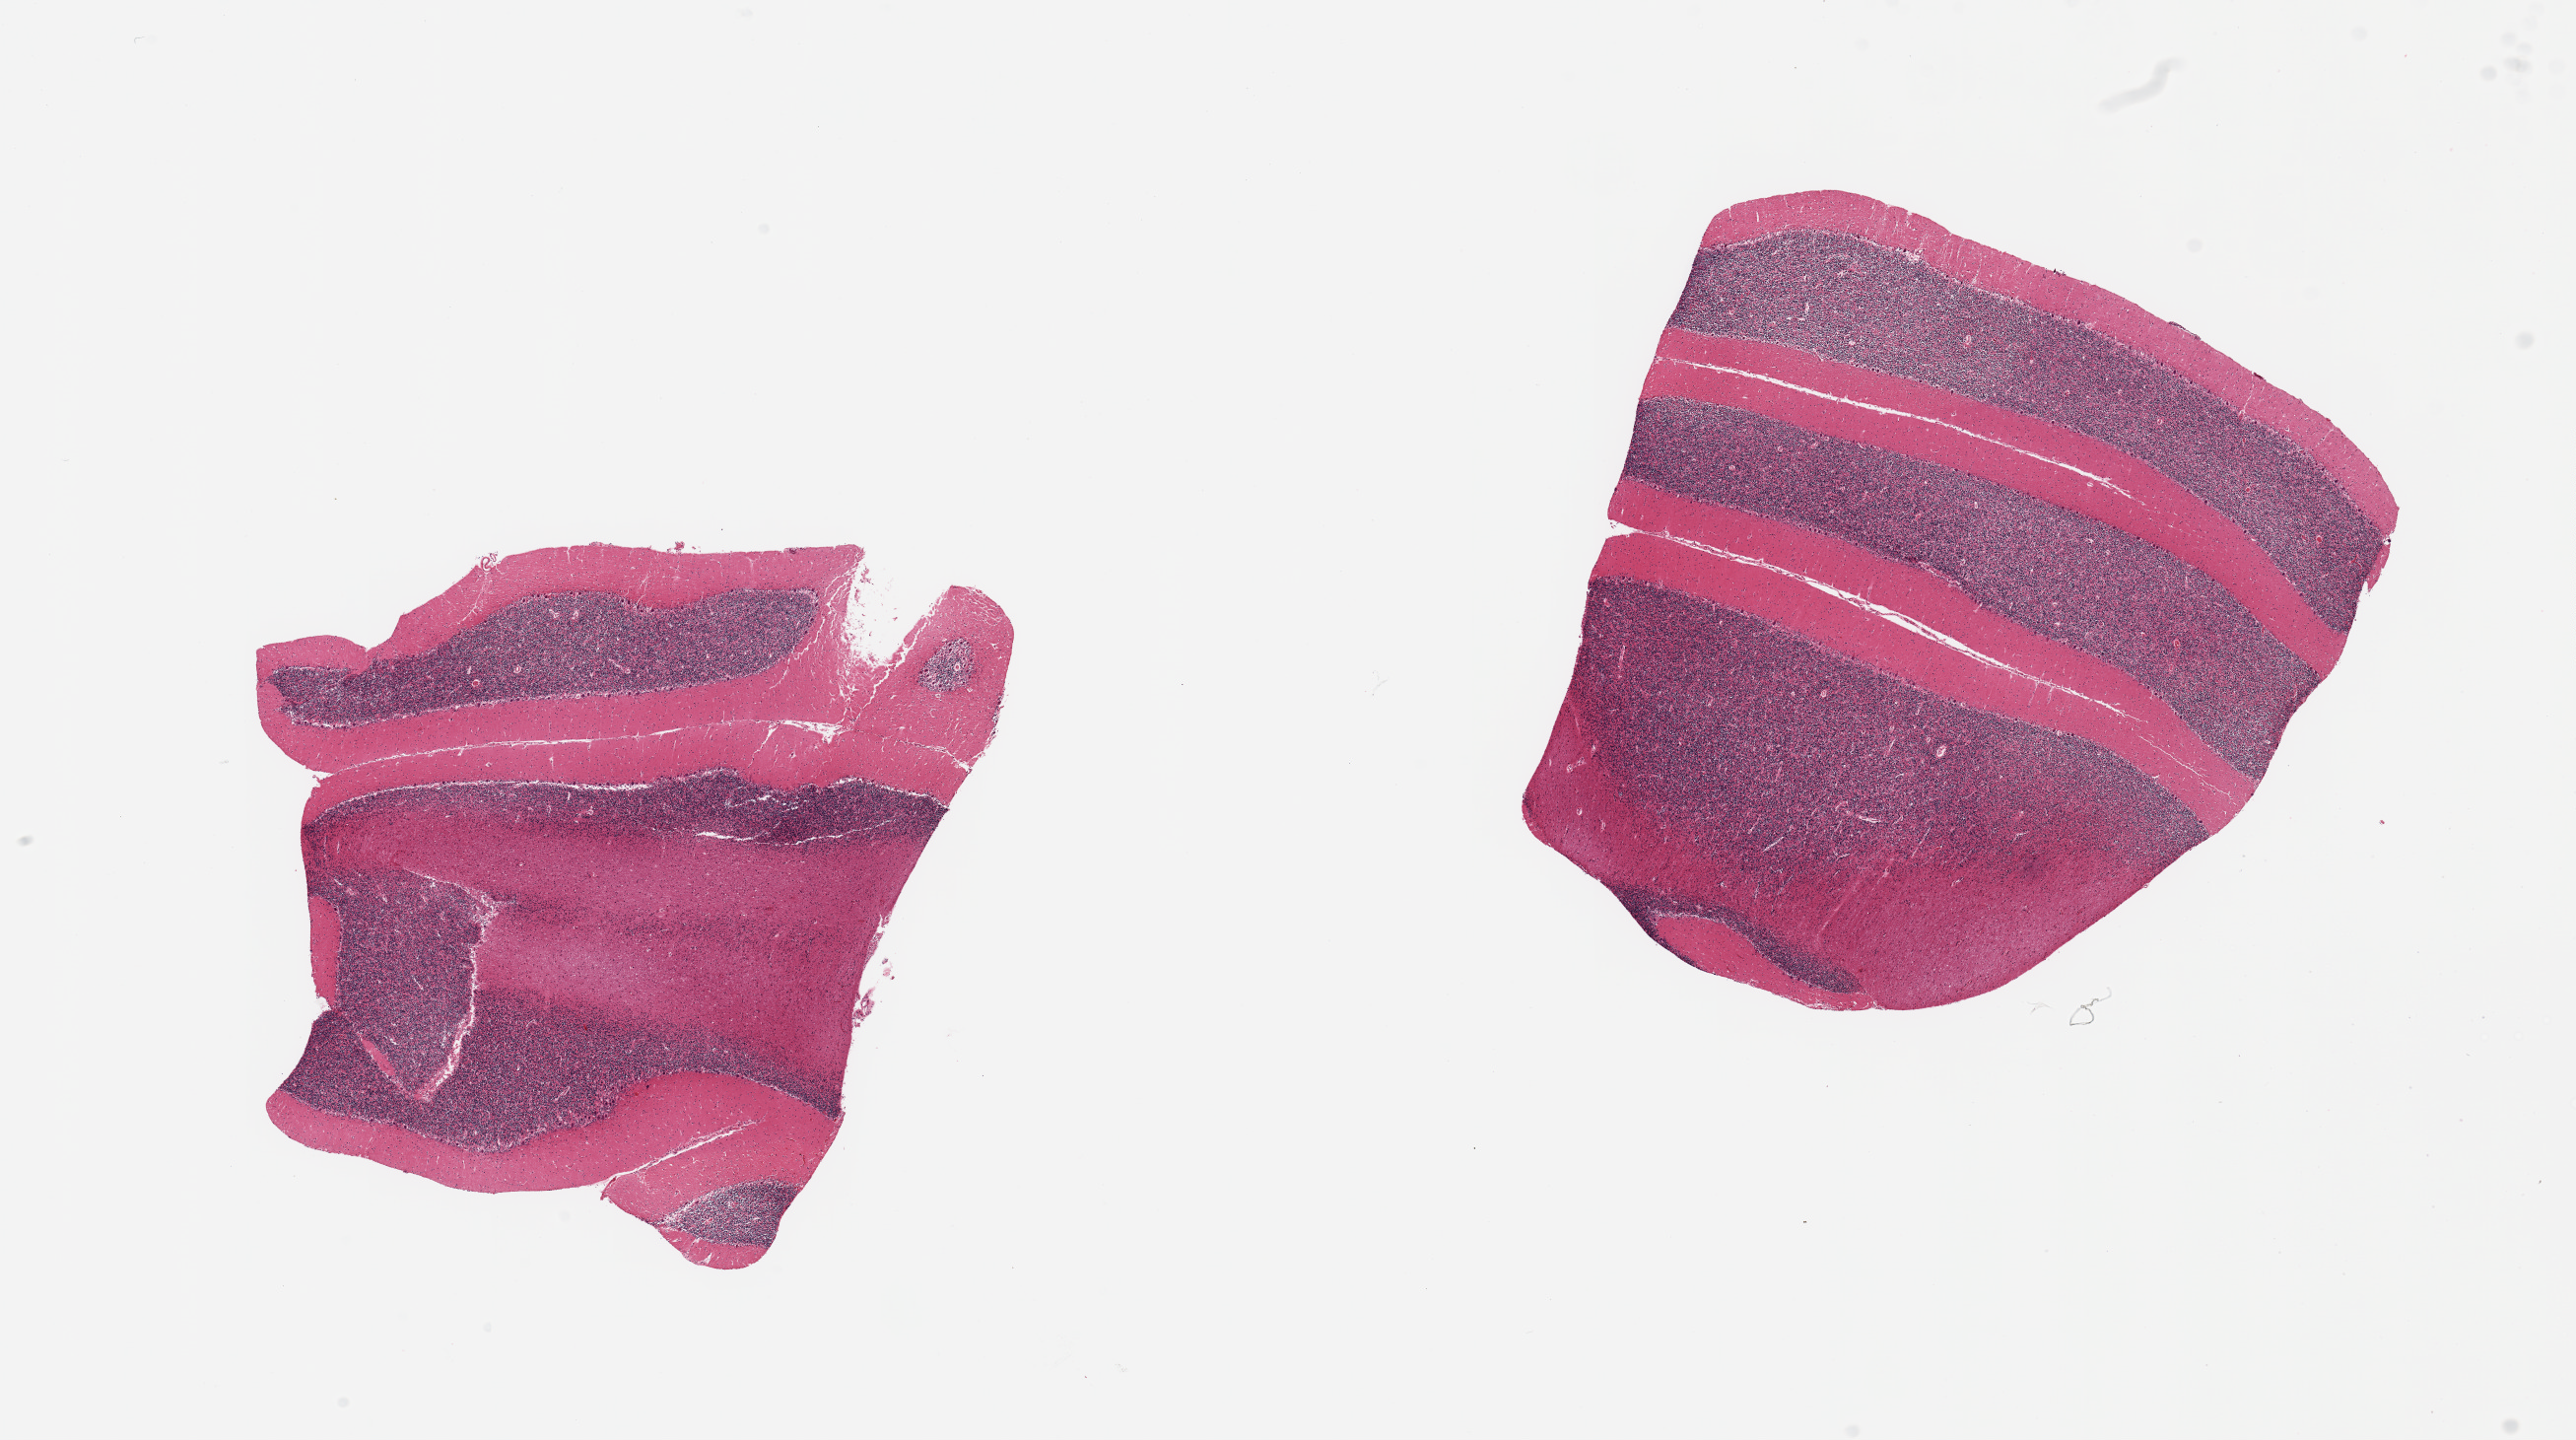
Whole-slide image, H&E stain, brightfield, whole scanned area (about 20.7 x 11.6 mm) shown as a low-resolution overview; PAXgene-fixed, paraffin-embedded tissue; sampled site (target tissue): cerebellum; donor tissue sample. Donor sex: female.
Review note (as recorded): 2 pieces.